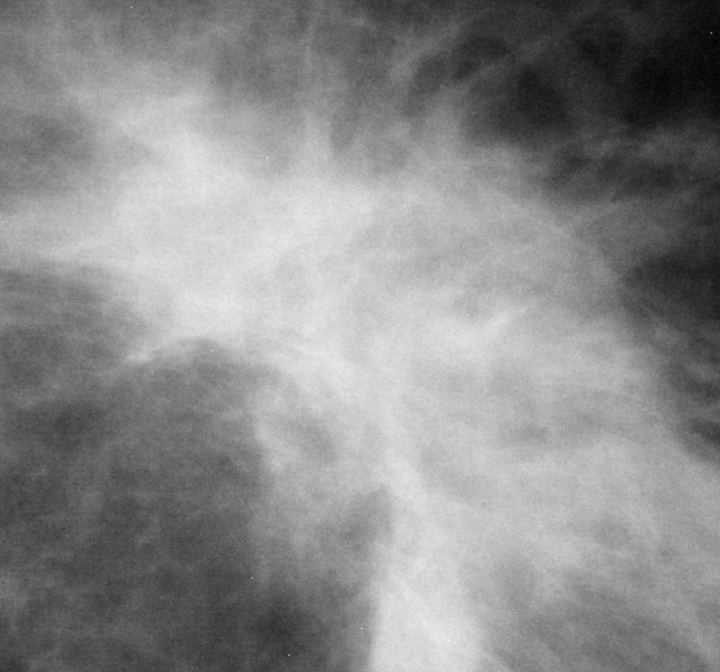
Region of interest cut from a scanned film mammogram (one marked finding); left breast; CC view.
Mass, shape irregular / architectural distortion, margins ill defined / spiculated; BI-RADS assessment category 4; pathology result (as recorded, not read from the image): malignant.